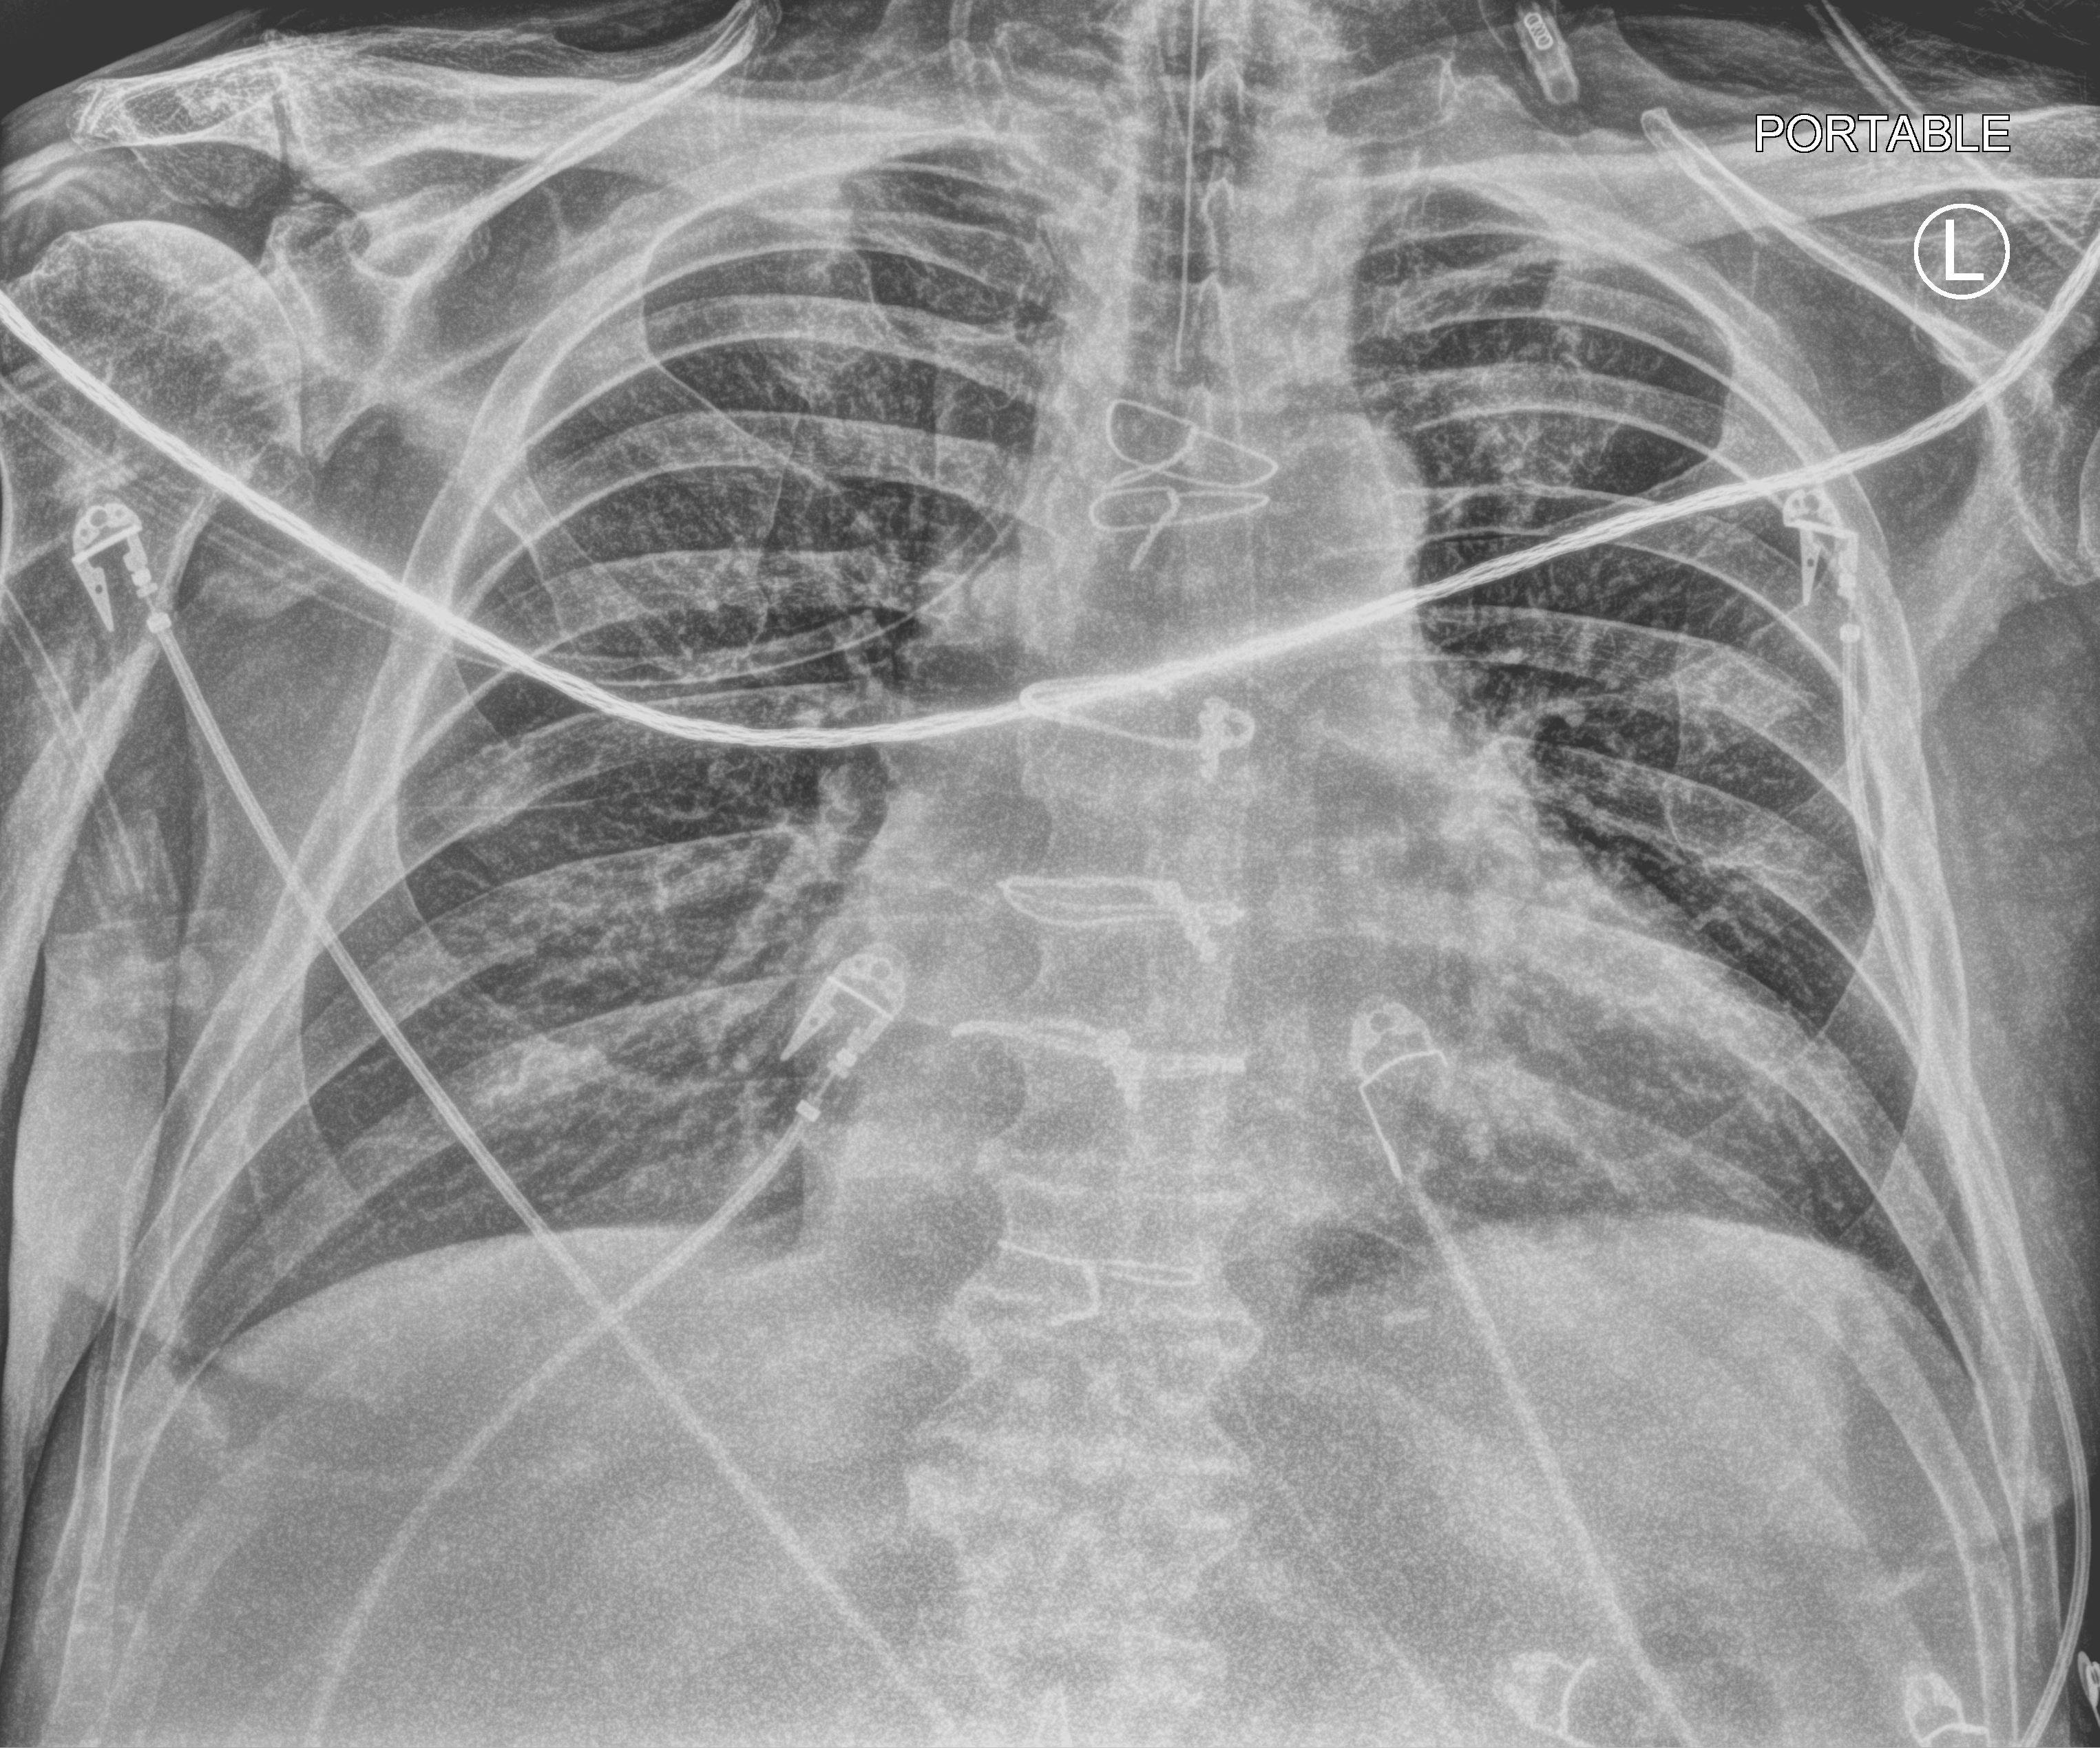
Portable chest radiograph; anteroposterior (AP) projection. Male patient hospitalised with COVID-19, age 60–74 years.
From the hospital-stay record, not from the radiograph (when in the stay this image was taken is not recorded): admitted to intensive care during this hospital stay: yes; length of hospital stay: 16 days; mechanically ventilated during this hospital stay: yes.